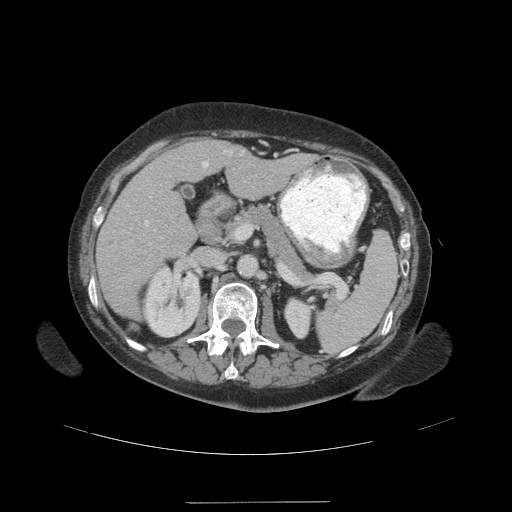
Contrast-enhanced abdominal CT (liver protocol), one axial slice. Position 56 of 99 along the scan axis. 140 kVp. Soft-tissue window (W 400 / L 40 HU). 512 × 512 image matrix, field of view 440 × 440 mm. Case-level facts recorded for this patient, not image findings: diagnosis: hepatocellular carcinoma (patient treated with transarterial chemoembolisation; whether this scan precedes or follows treatment is not stated here); TNM stage (as recorded): Stage-IVA; Child-Pugh class: A.
Structures marked on this image (semi-automatically segmented with operator editing):
- liver parenchyma outside the tumour (the mass and vessels are separate outlines, so this box may not span the whole liver): box from (x=96, y=142) to (x=312, y=318) px
- liver vessels: (x=145, y=150)–(x=232, y=227)